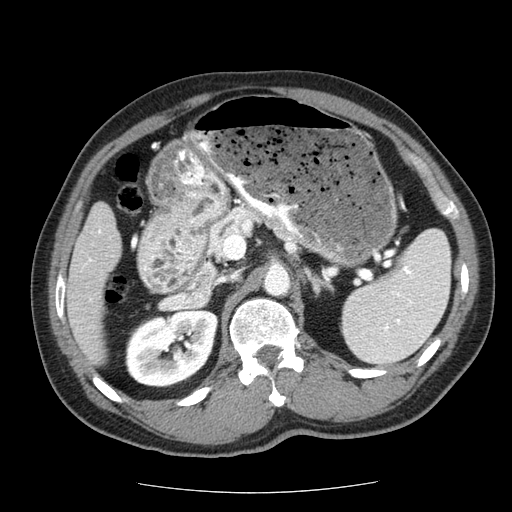
Contrast-enhanced abdominal CT (liver protocol), one axial slice. Slice 21 of 85 in the series (ordered by position). Soft-tissue window (W 400 / L 40 HU). 512 × 512 image matrix, field of view 360 × 360 mm. From the clinical record (not read from this slice): diagnosis: hepatocellular carcinoma (patient treated with transarterial chemoembolisation; whether this scan precedes or follows treatment is not stated here); TNM stage (as recorded): Stage-IIIA; Child-Pugh class: A; tumour differentiation: well differentiated; tumour nodularity: multinodular.
Outlined on this slice (semi-automatic segmentation, software-assisted and operator-edited):
- liver parenchyma outside the tumour (the mass and vessels are separate outlines, so this box may not span the whole liver): bounding box [x1, y1, x2, y2] px = [66, 202, 120, 364]
- liver vessels: [85, 230, 101, 265]